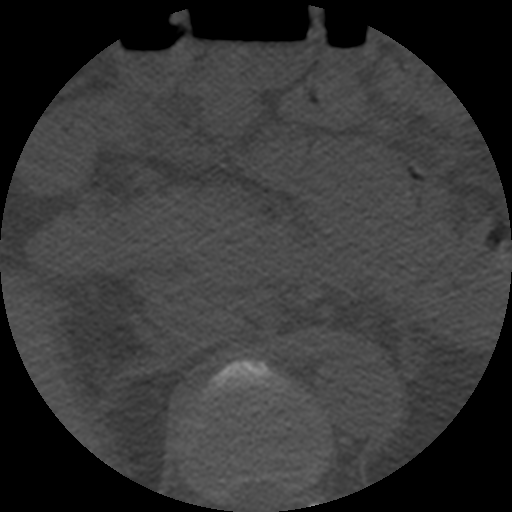
CT including the spine, one axial slice. Position 228 of 508 along the scan axis. 120 kVp. Bone window (W 1800 / L 400 HU). 1.25 mm slice thickness. 512 × 512 image matrix. Patient age 57 years. Case-level facts recorded for this patient, not image findings: primary cancer: prostate.
Outlined on this slice (semi-automatic segmentation, software-assisted and operator-edited):
- T11 vertebra: bounding box (x1, y1, x2, y2) in pixels: (217, 467, 317, 495)
- T12 vertebra: (203, 360, 287, 480)